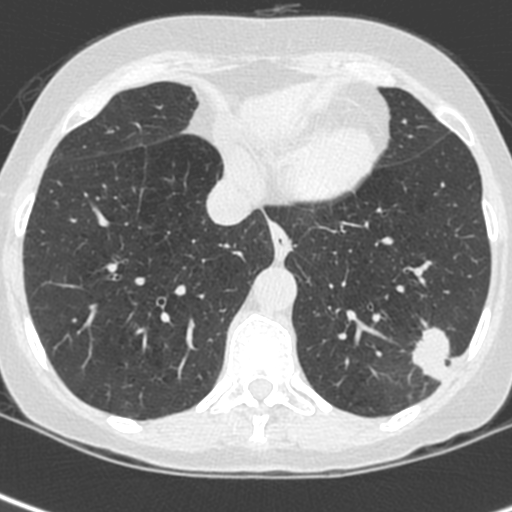
Chest CT (low-dose screening protocol), one axial image. Baseline annual screen. Lung window (W 1500 / L -600 HU). 512 × 512 image matrix, field of view 271 × 271 mm. Female participant, aged 56 years at enrolment.
• Lesion marked by an expert reader, bounding box (x1, y1, x2, y2) in pixels: (408, 323, 474, 389).
• Screening reader's record for this exam (one nodule recorded; not confirmed to be the boxed lesion): non-calcified nodule or mass ≥4 mm, left lower lobe, 37 × 29 mm, spiculated (stellate) margins, ground glass attenuation.
• Official screen result: positive, change unspecified: nodule(s) >= 4 mm or enlarging nodule(s), mass(es), or other non-specific abnormalities suspicious for lung cancer.
• Lung cancer was diagnosed 91 days after this screen: squamous cell carcinoma, NOS, left lower lobe, poorly differentiated (G3), stage IIIA (AJCC 6th edition), 35 mm at pathology.